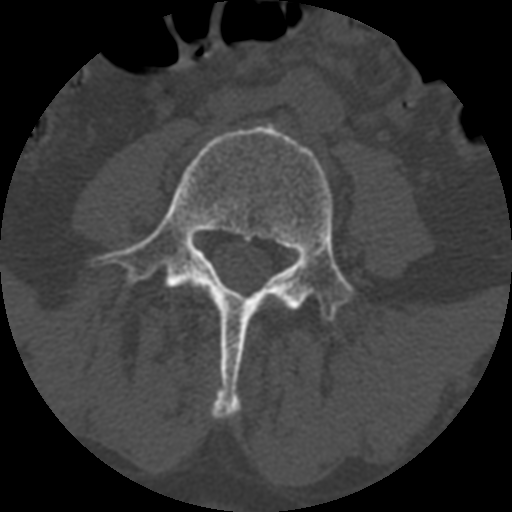
CT including the spine, one axial slice; slice 283 of 399 in the series (ordered by position); bone window (W 1800 / L 400 HU); 1.25 mm slice thickness; 512 × 512 image matrix, field of view 160 × 160 mm. Patient age 71 years. Case-level facts recorded for this patient, not image findings: primary cancer: prostate.
Structures marked on this image (semi-automatically segmented with operator editing):
- L4 vertebra: bounding box (x1, y1, x2, y2) in pixels: (97, 123, 358, 418)